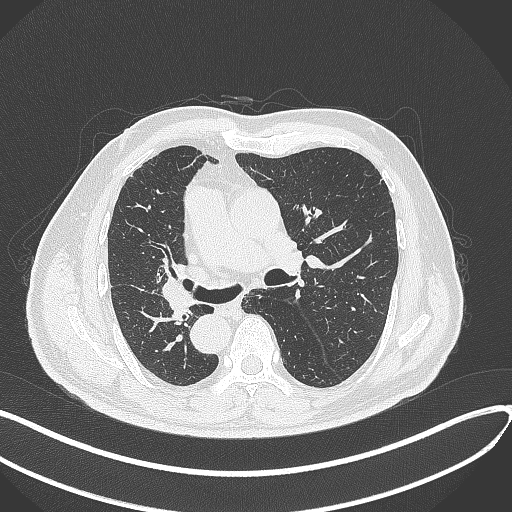
Chest CT, one axial slice; slice 169 of 300 in the series (ordered by position); 120 kVp; lung window (W 1500 / L -600 HU); 1 mm slice thickness; 512 × 512 image matrix, field of view 400 × 400 mm. Patient: male, 67 years. Case-level facts recorded for this patient, not image findings: clinical TNM (as recorded): T2a N0 M0.
Structures marked on this image (bounding box drawn by a radiologist):
- lung tumour (recorded histology: squamous cell carcinoma): bounding box [x1, y1, x2, y2] px = [160, 275, 199, 330]